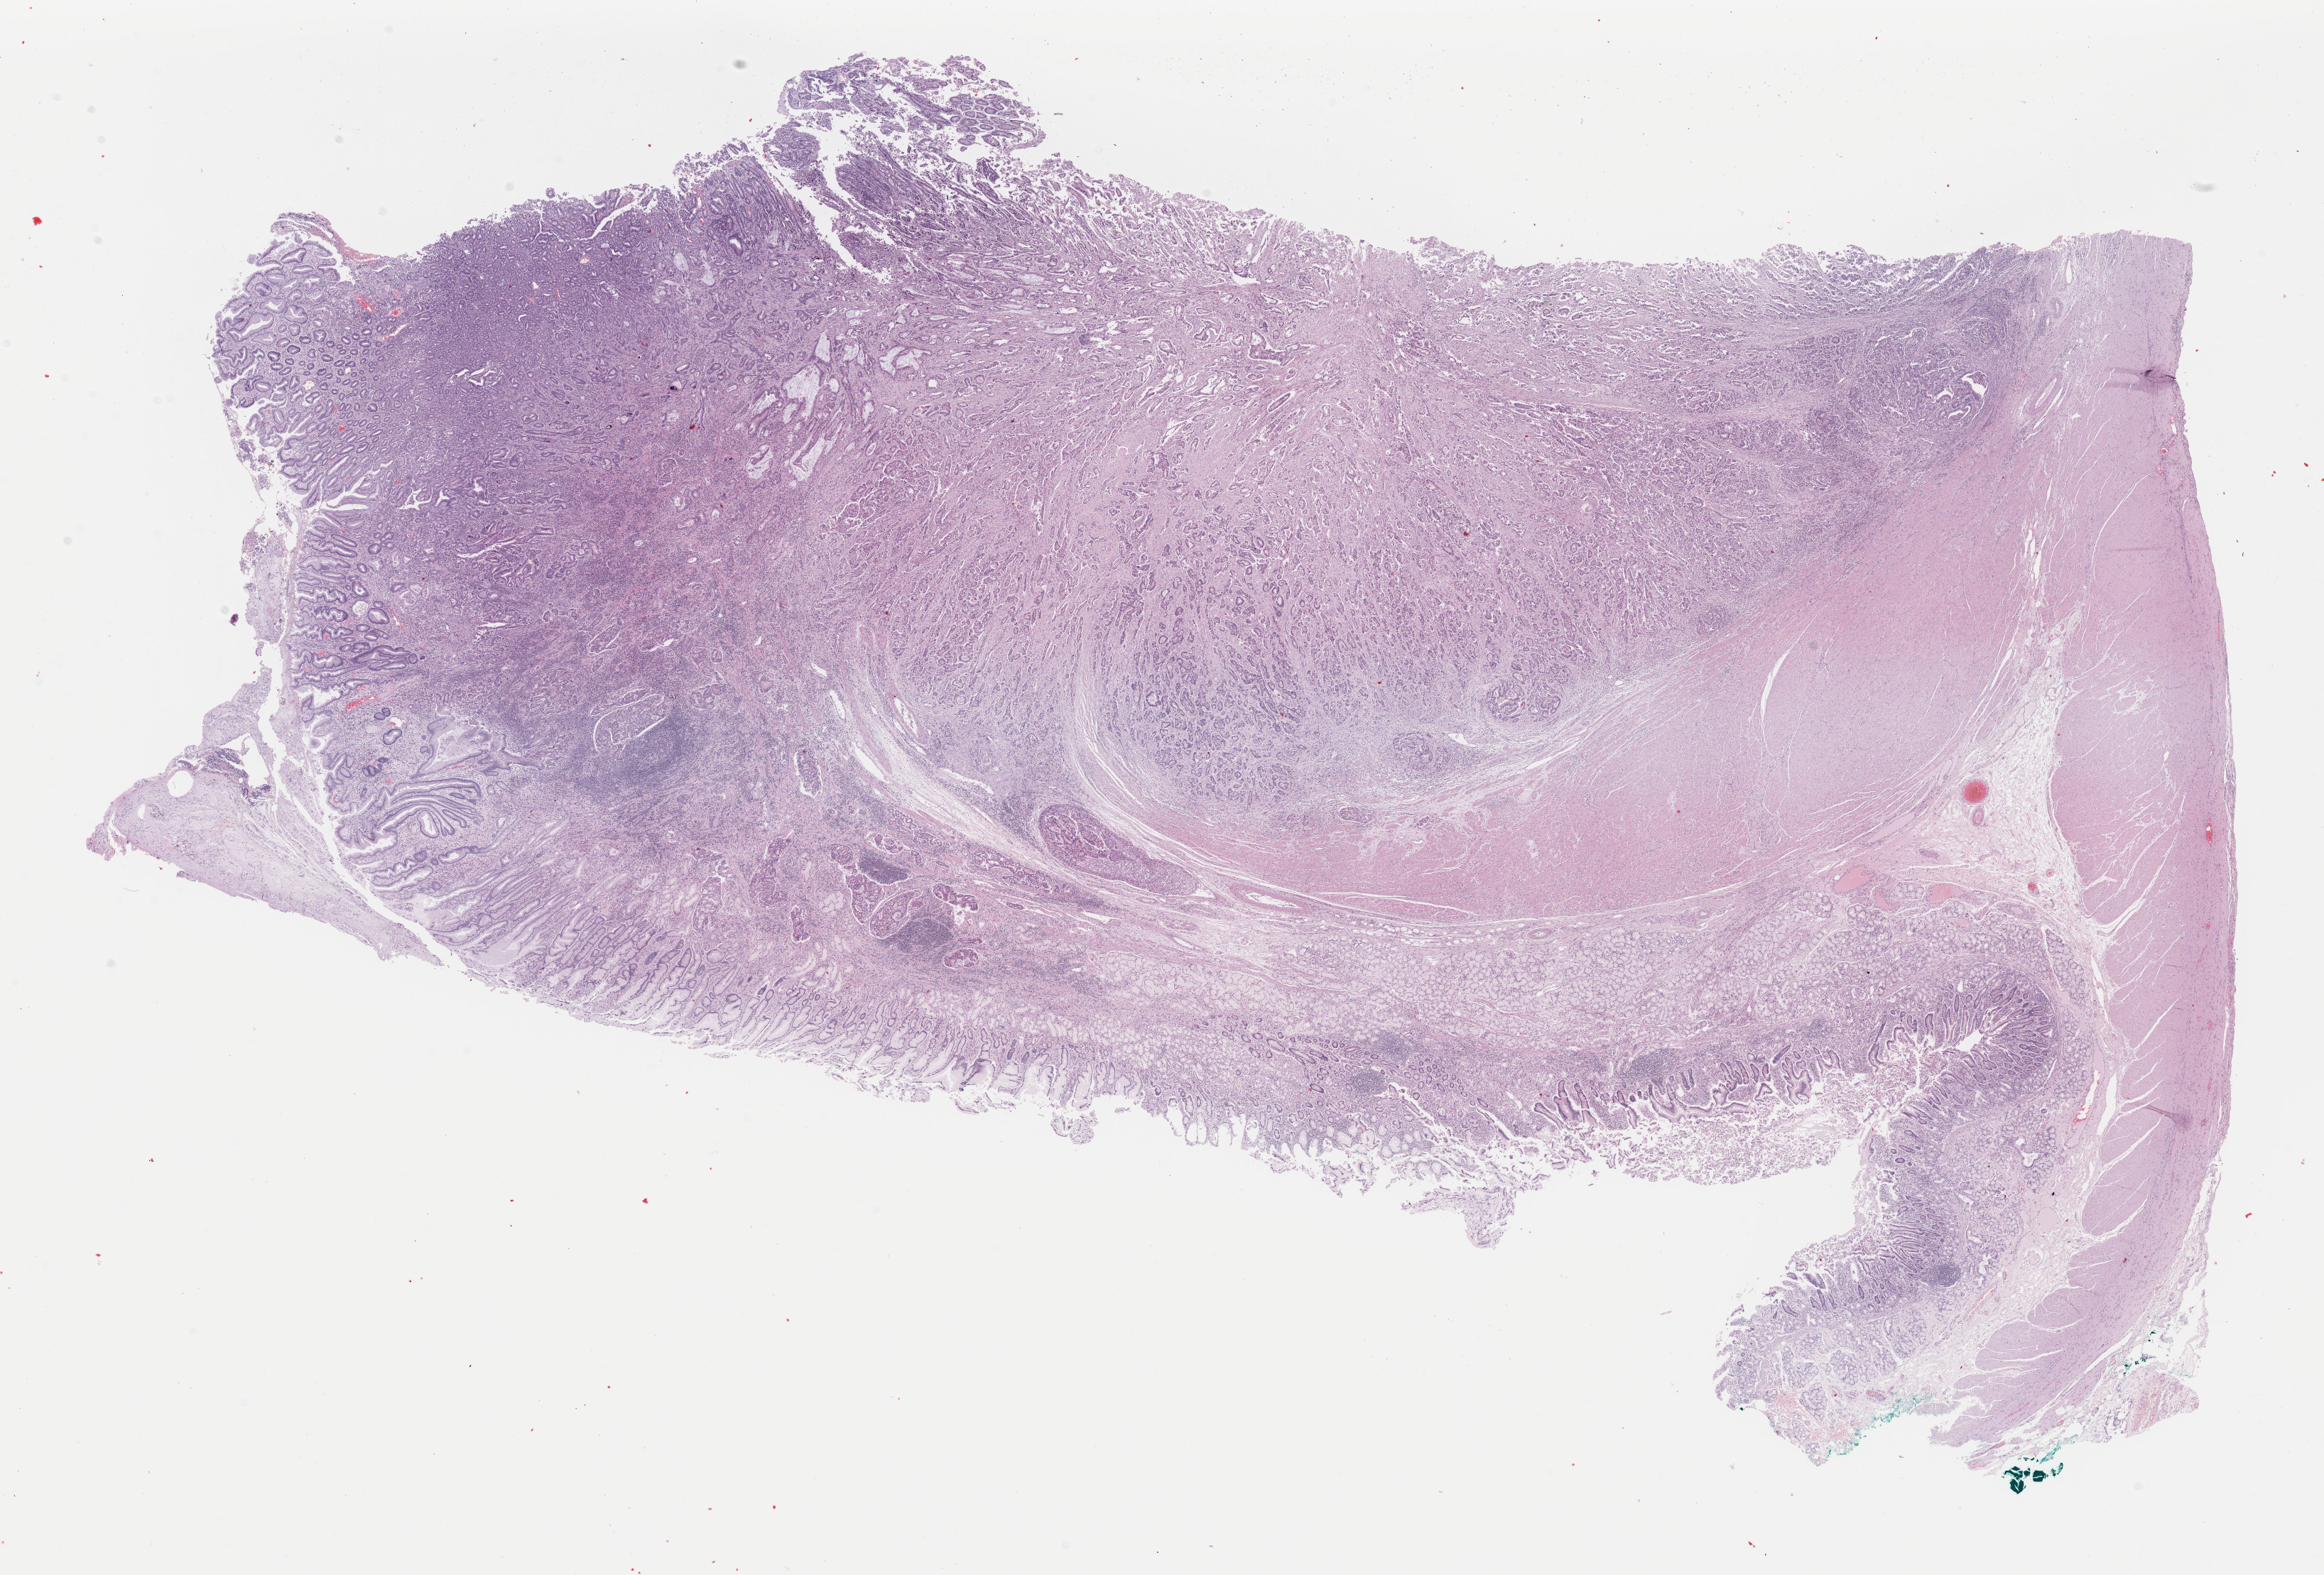
Hematoxylin and eosin (H&E) stained whole-slide image — low-resolution overview of the scanned area, about 25.8 x 17.5 mm (slide scanned at 40x), FFPE section, stomach, primary tumour sample. Patient: male, age at initial diagnosis 61 years. Histologic grade: G3 (poorly differentiated).
* AJCC pathologic stage: IIIB (7th edition)
* TNM: T3 N3a M0
* diagnosis: Adenocarcinoma, NOS
* lymph nodes positive (case pathology): 7 of 22 examined